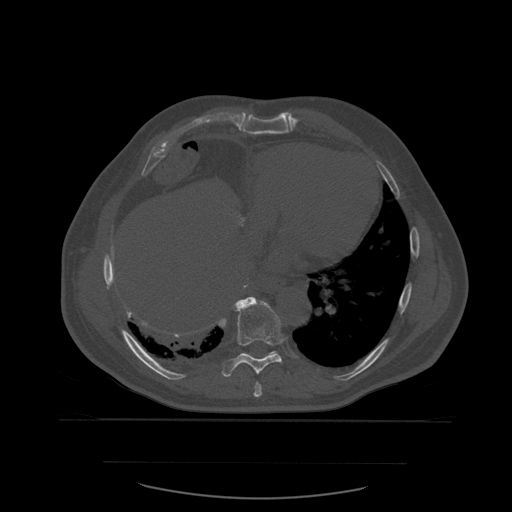
CT including the spine, one axial slice; slice 338 of 590 in the series (ordered by position); bone window (W 1800 / L 400 HU); 1.25 mm slice thickness; 512 × 512 image matrix, field of view 479 × 479 mm. Patient age 71 years. Case-level facts recorded for this patient, not image findings: primary cancer: lung.
Structures marked on this image (semi-automatically segmented with operator editing):
- T8 vertebra: box from (x=254, y=382) to (x=263, y=398) px
- T9 vertebra: (x=220, y=297)–(x=283, y=377)